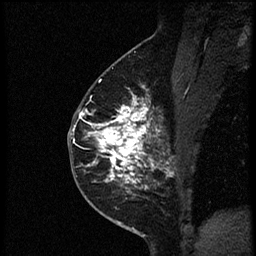
Breast MRI (dynamic contrast-enhanced), one sagittal slice. Position 34 of 56 along the scan axis. Dynamic contrast-enhanced study with each time point stored as its own series, time point 2 of 4 at this slice position (early post-contrast, ordered by acquisition time). 1.5 T. TE 4.2 ms, TR 18.9 ms. 256 × 256 image matrix. Female patient. From the clinical record (not read from this slice): setting: breast cancer imaged before/during neoadjuvant chemotherapy; receptor status: HER2-positive.
Structures marked on this image (semi-automatically segmented with operator editing):
- analysis volume of interest (the breast-tissue region the enhancement analysis was run in; not a lesion): bounding box [x1, y1, x2, y2] px = [78, 85, 173, 189]
- tumour enhancement mask (voxels above the 100 % enhancement threshold inside the analysis volume of interest): [82, 95, 166, 189]